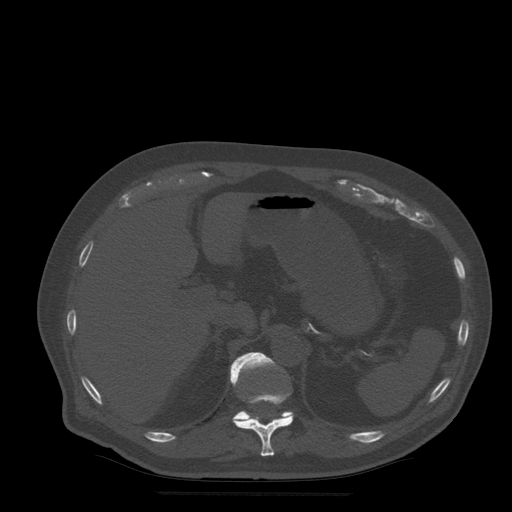
CT including the spine, one axial slice. Slice 236 of 522 in the series (ordered by position). Bone window (W 1800 / L 400 HU). 1.25 mm slice thickness. 512 × 512 image matrix, field of view 420 × 420 mm. Patient age 72 years. From the clinical record (not read from this slice): primary cancer: prostate.
Annotated regions visible in this slice (semi-automatic segmentation, software-assisted and operator-edited):
- T11 vertebra: bounding box [x1, y1, x2, y2] px = [233, 393, 294, 457]
- T12 vertebra: [230, 352, 293, 420]